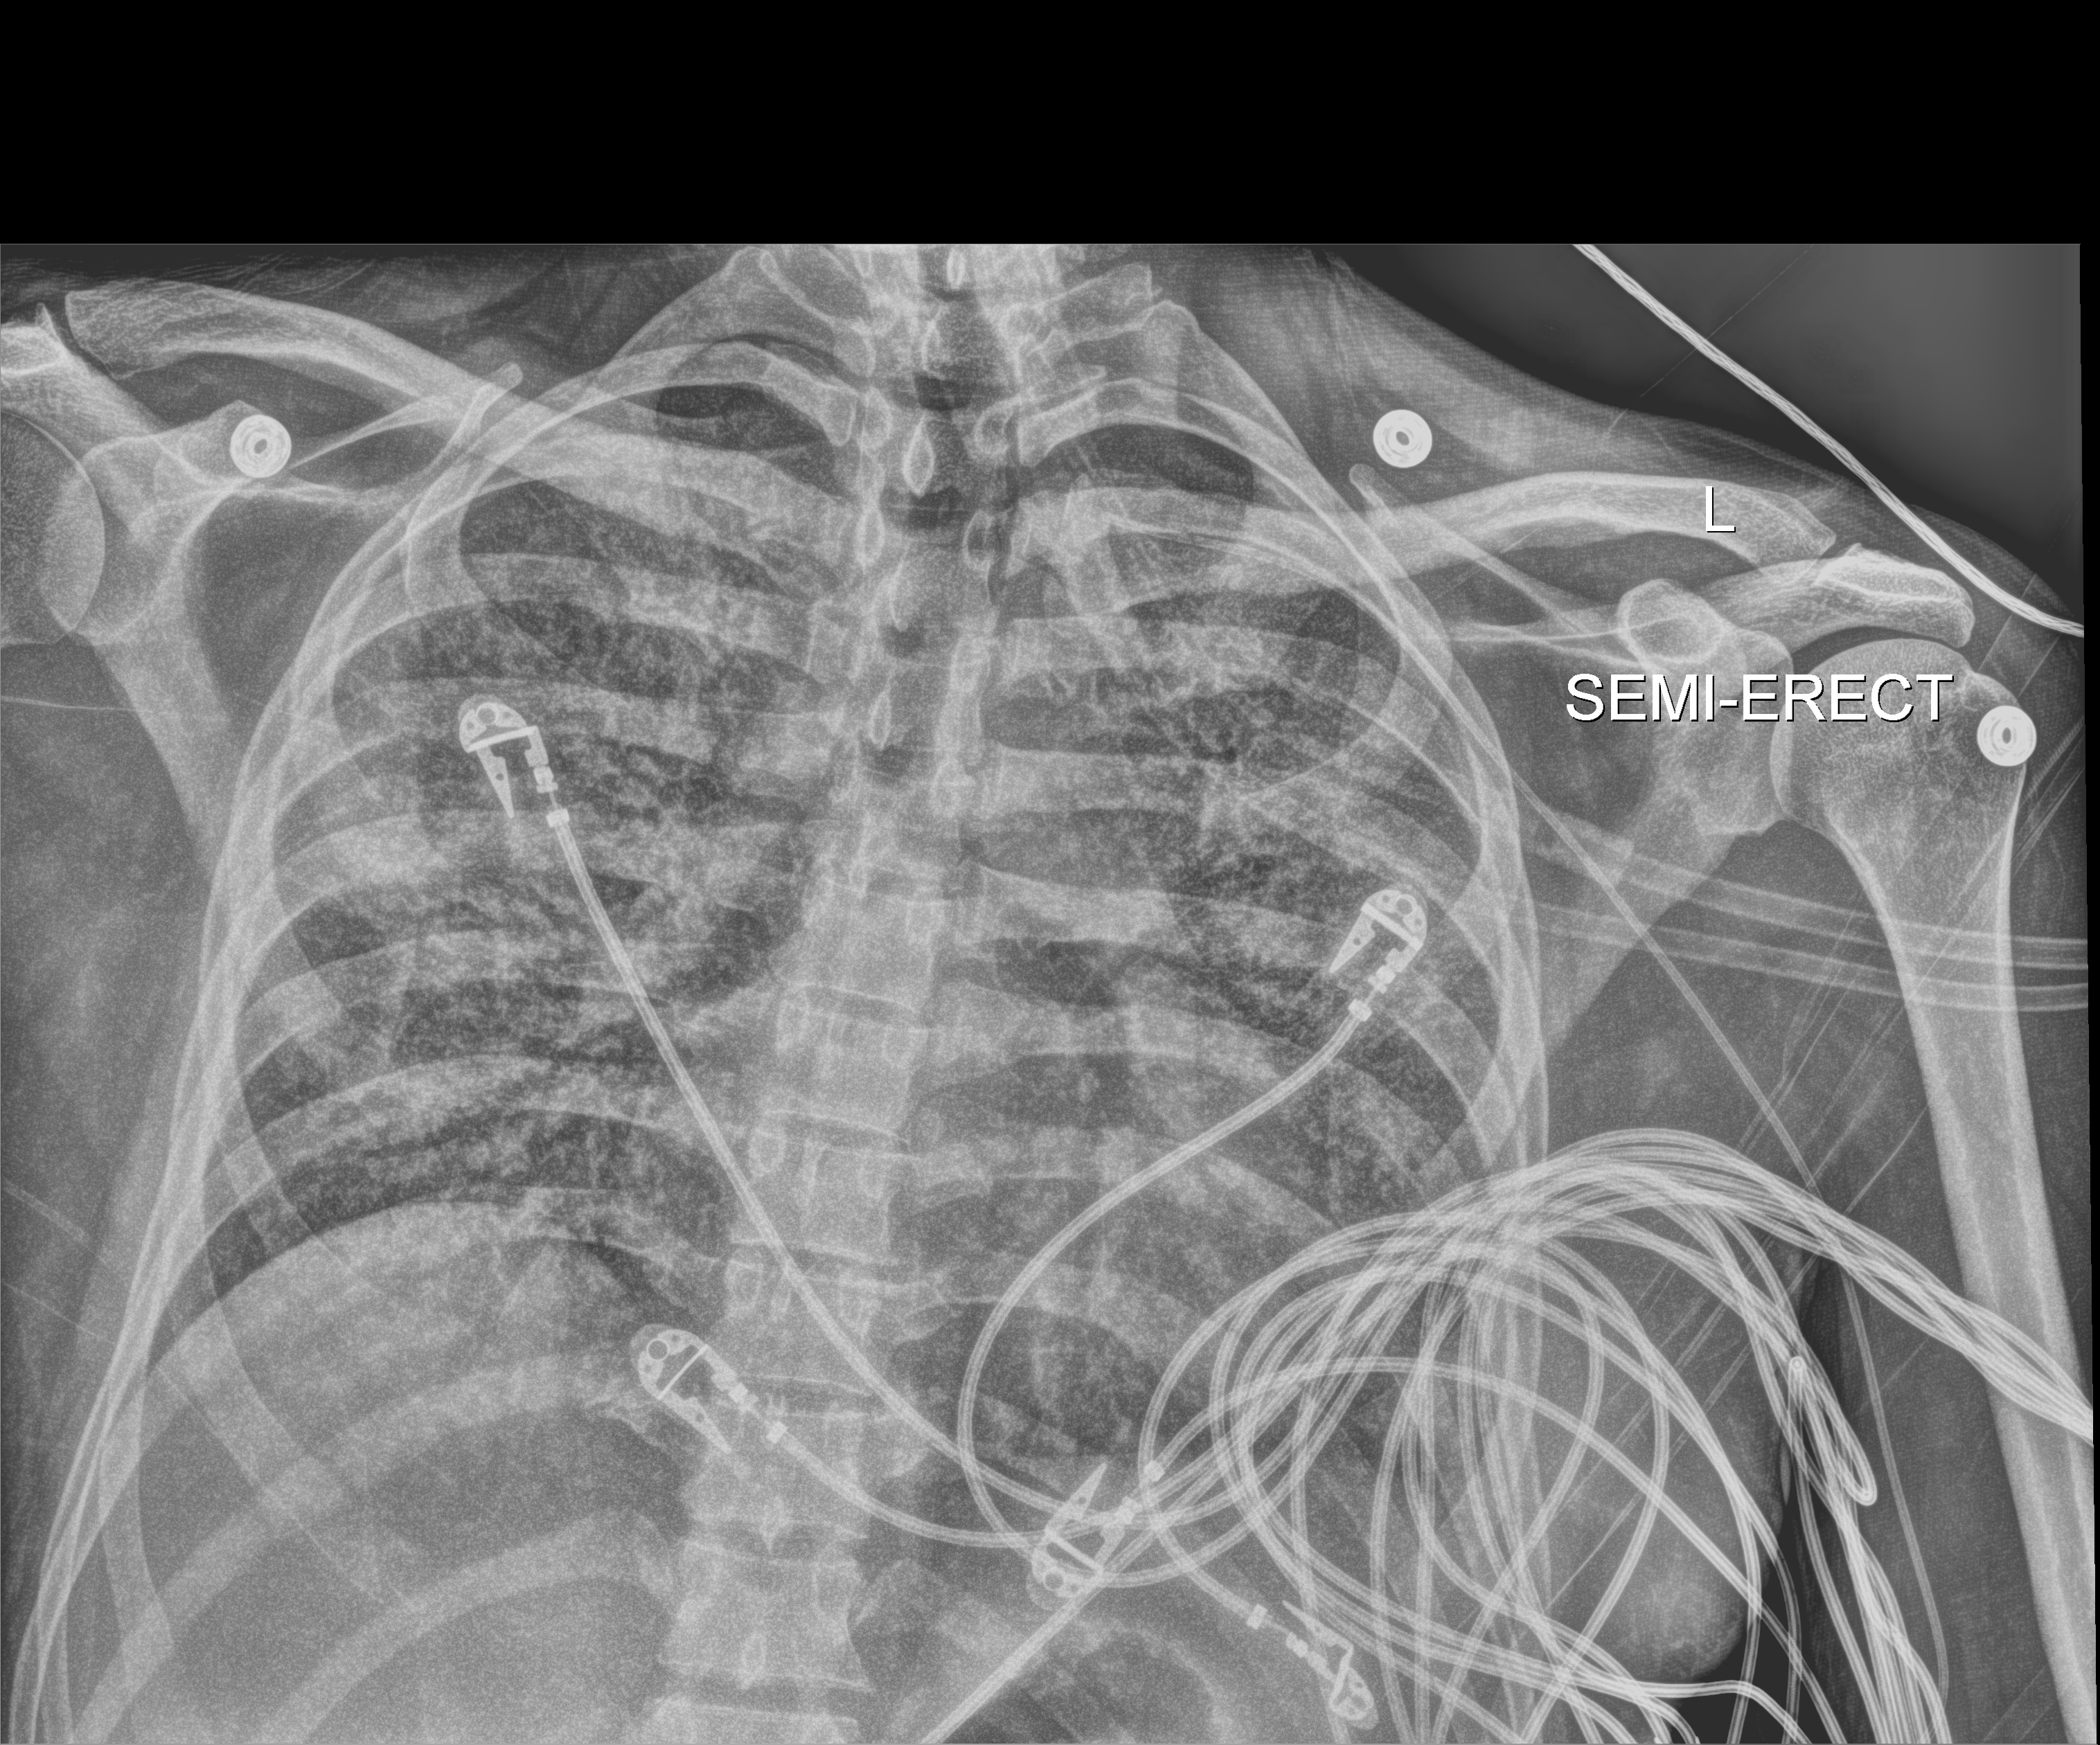
Bedside chest radiograph (digital radiography); anteroposterior (AP) projection. Male patient hospitalised with COVID-19, age 18–59 years.
Hospital-stay facts (about this admission, not read from this image; timing relative to this image not recorded): other chronic lung disease (admission record): no.